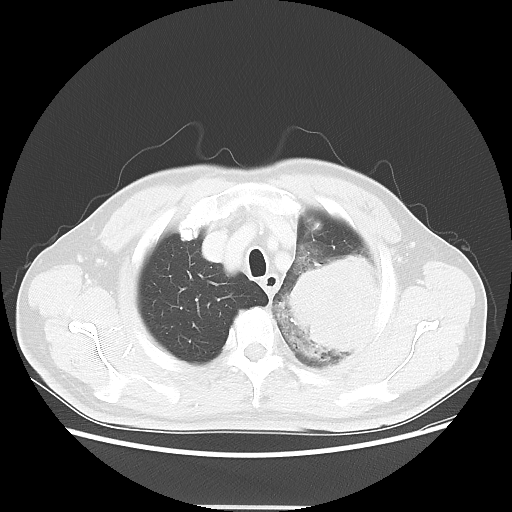
Chest CT, one axial slice. Position 47 of 53 along the scan axis. Reconstruction kernel LUNG. Lung window (W 1500 / L -600 HU). 5 mm slice thickness. 512 × 512 image matrix. Patient: male, 60 years. Case-level facts recorded for this patient, not image findings: clinical TNM (as recorded): T4 N1 M1a.
Annotated regions visible in this slice (rectangle marked by the reading radiologist):
- lung tumour (recorded histology: large cell carcinoma): bounding box (x1, y1, x2, y2) in pixels: (284, 256, 377, 354)